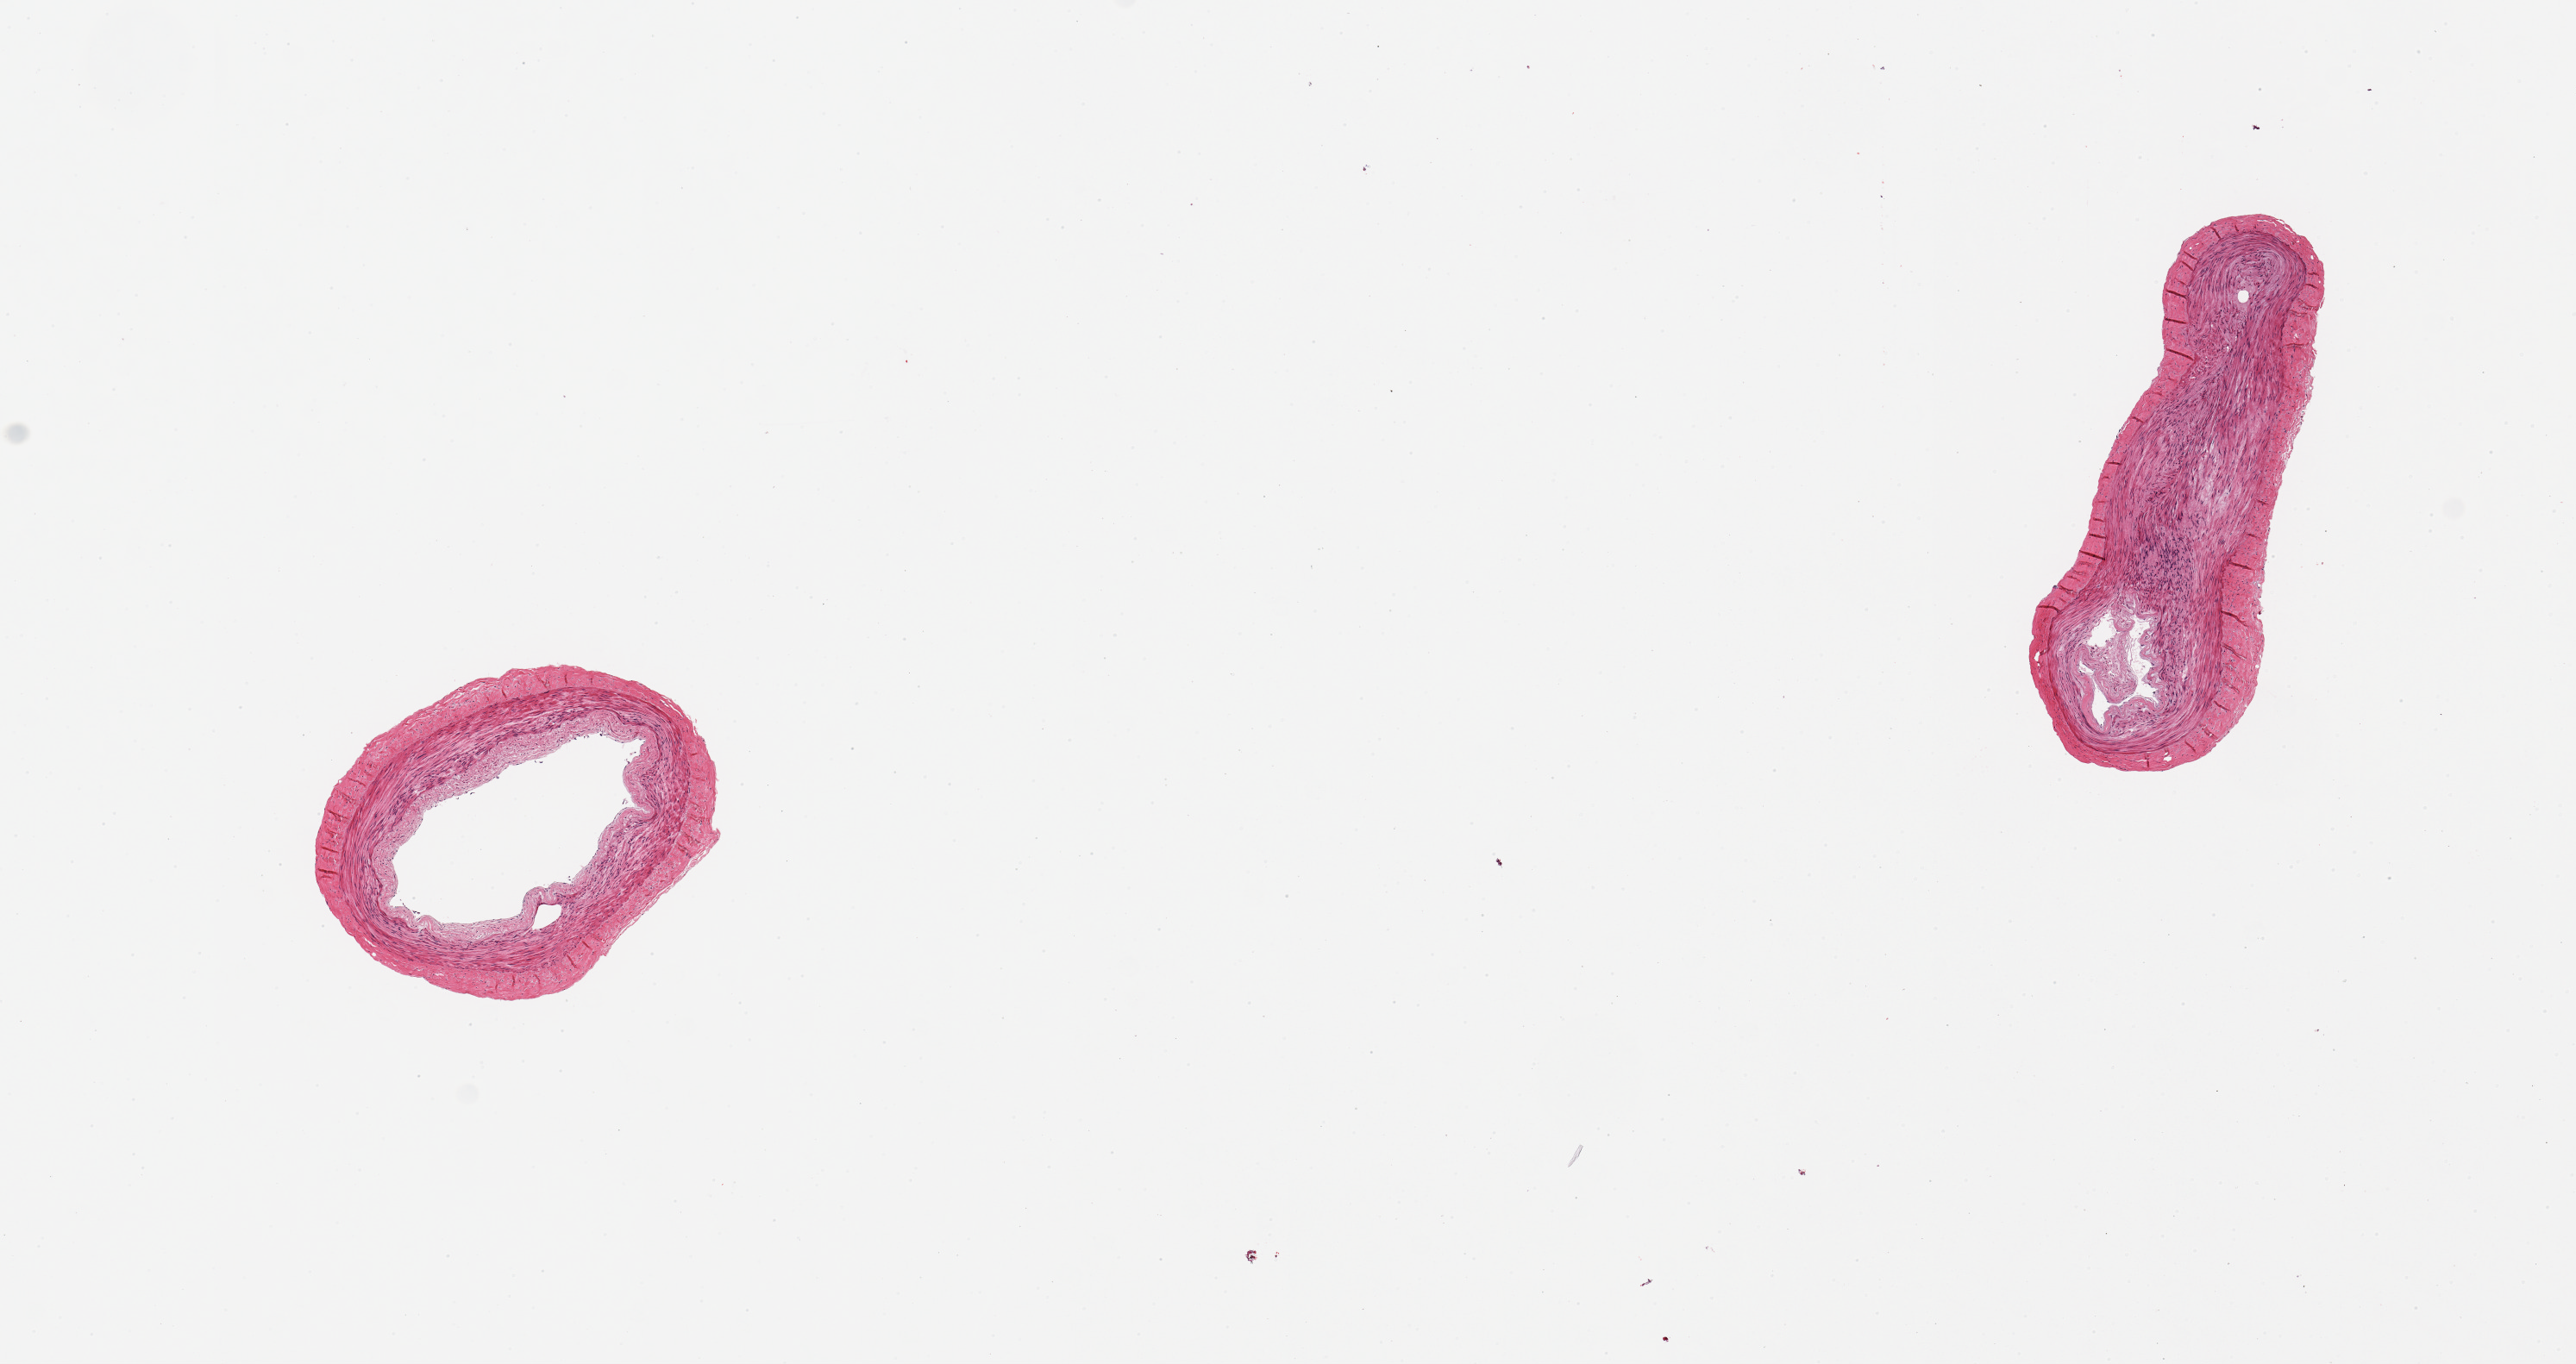
Whole-slide image, hematoxylin and eosin (H&E) stain, shown as a low-resolution overview of the whole scanned area (about 11.8 x 6.3 mm, from a 20x scan); PAXgene-fixed paraffin-embedded (PFPE) section; sampled site (target tissue): tibial artery; donor tissue sample. Donor sex: female.
Pathologist's review note for this sample: 2 pieces; well trimmed; no lesions.